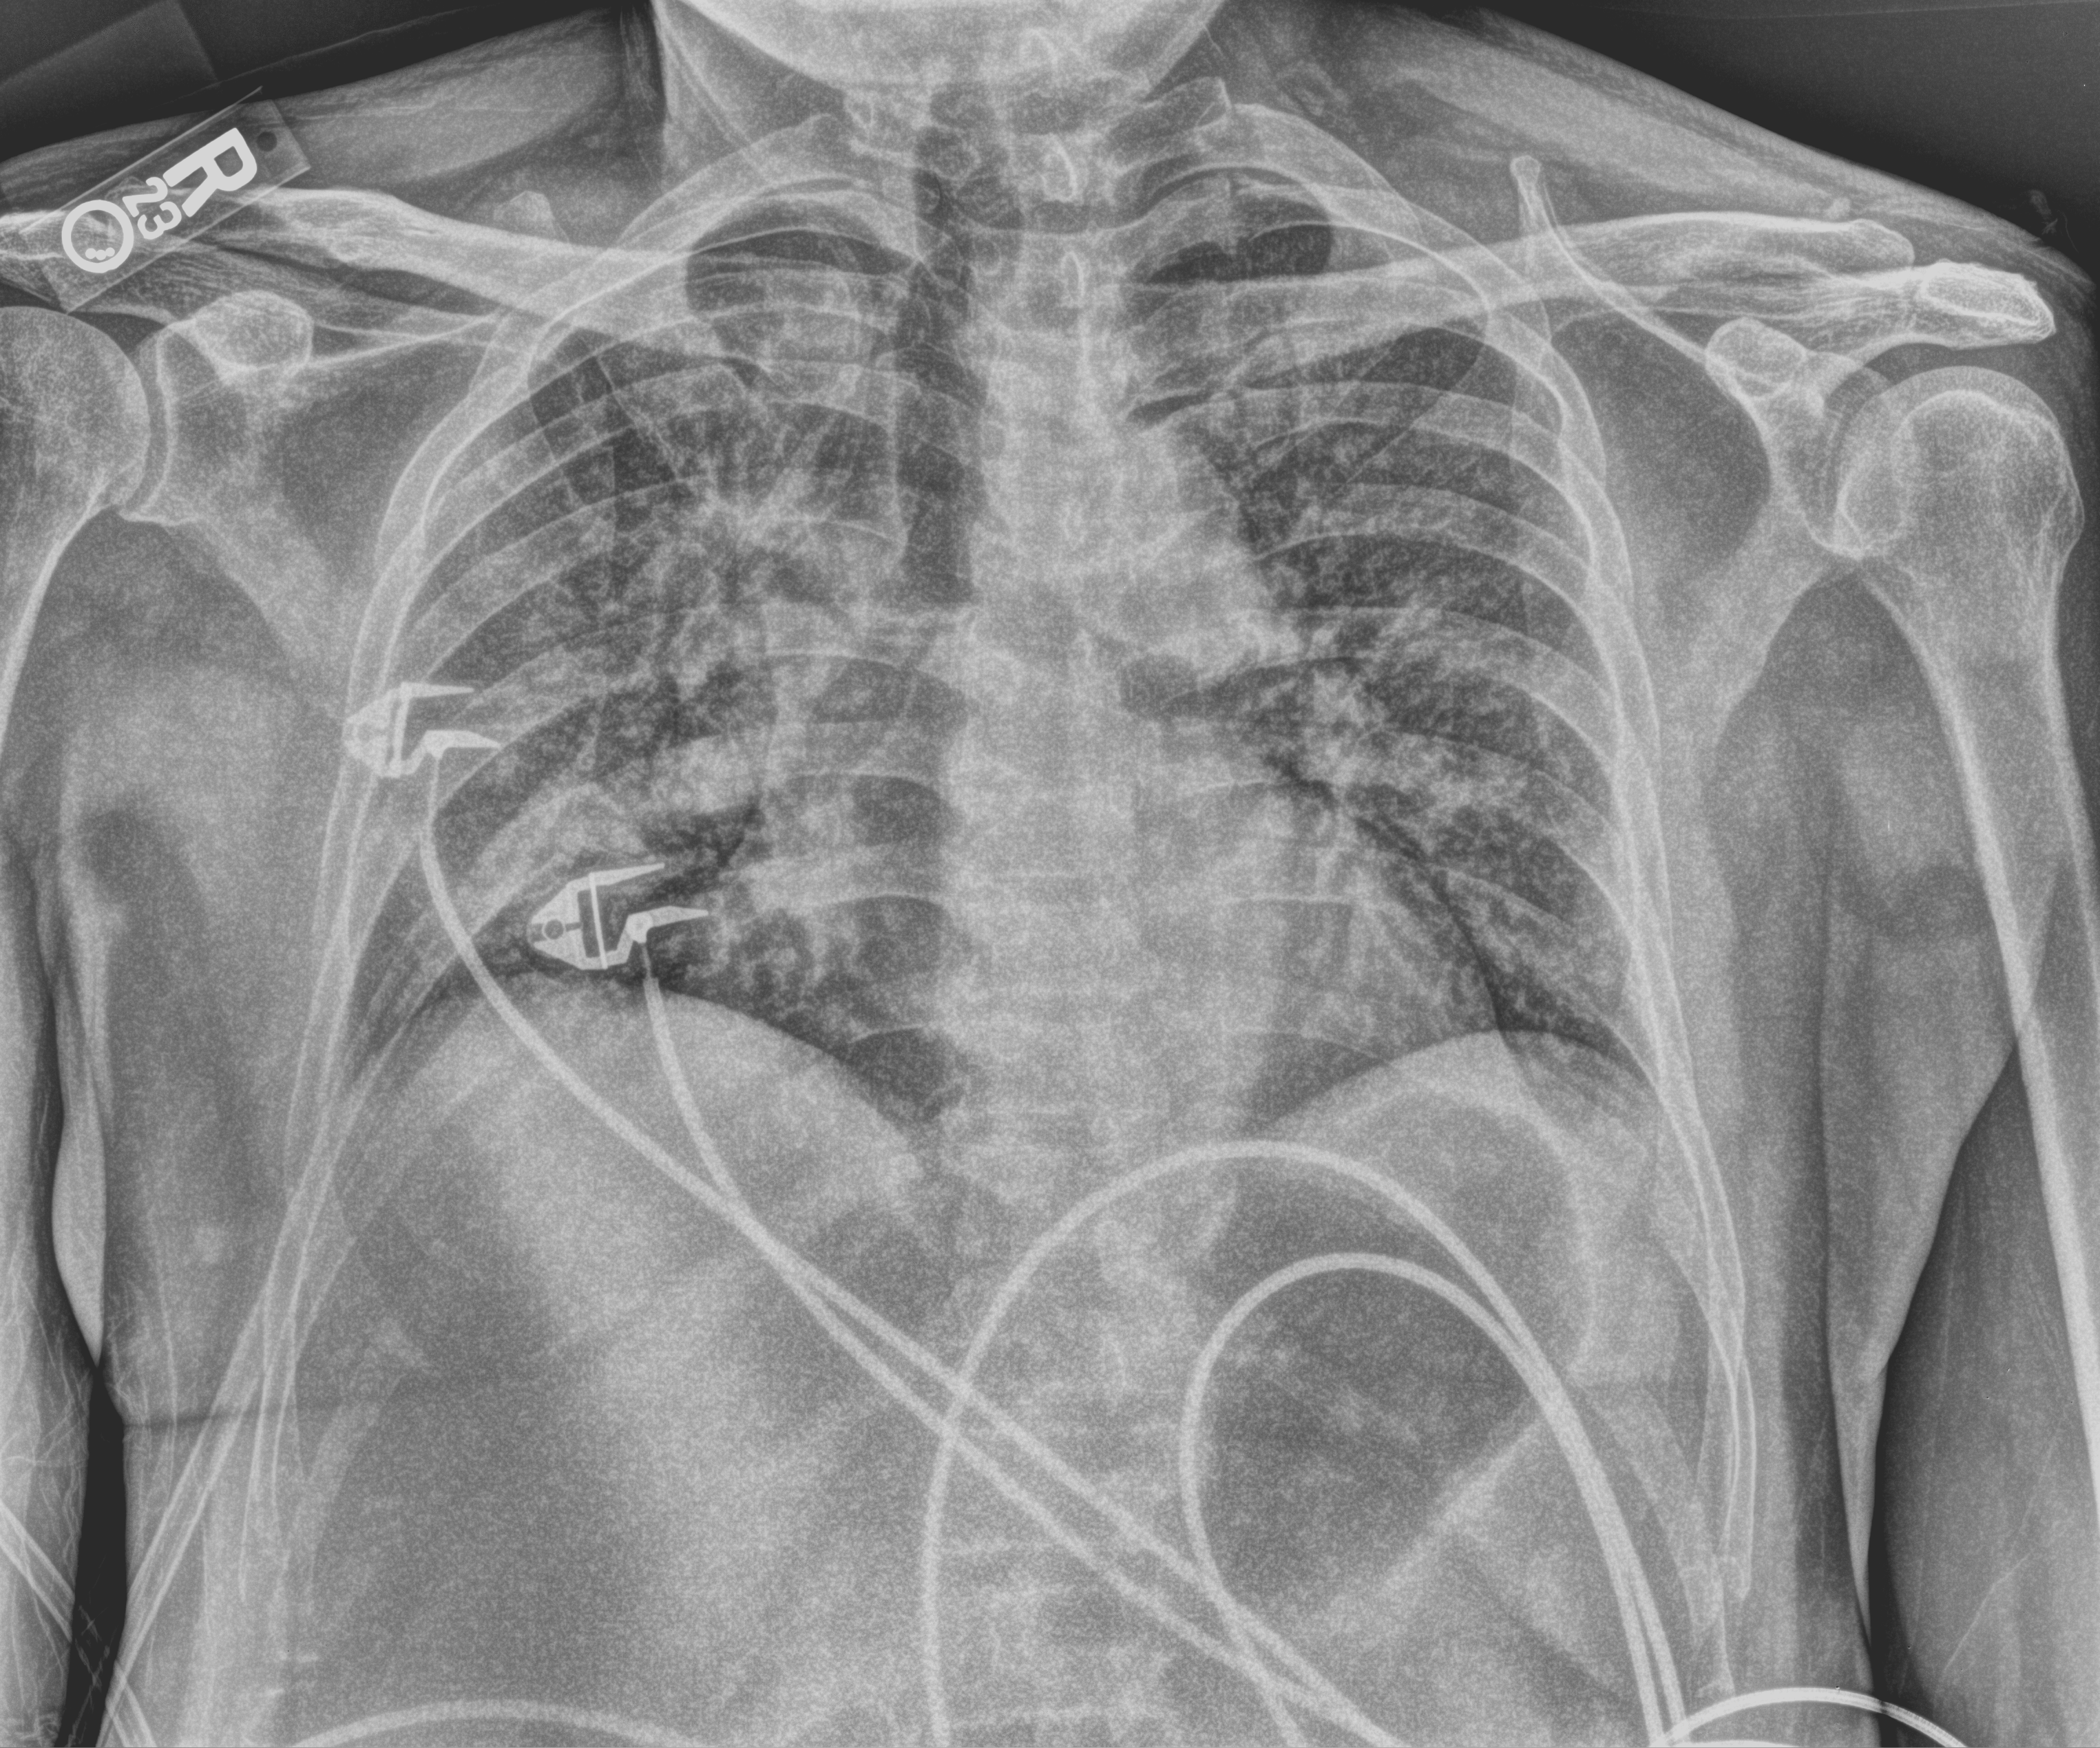
Portable chest radiograph. Patient hospitalised with COVID-19; male, aged 60–74 years.
Admission-level facts for this patient (not findings on this image; timing relative to this image not recorded): chronic kidney disease (admission record): no.